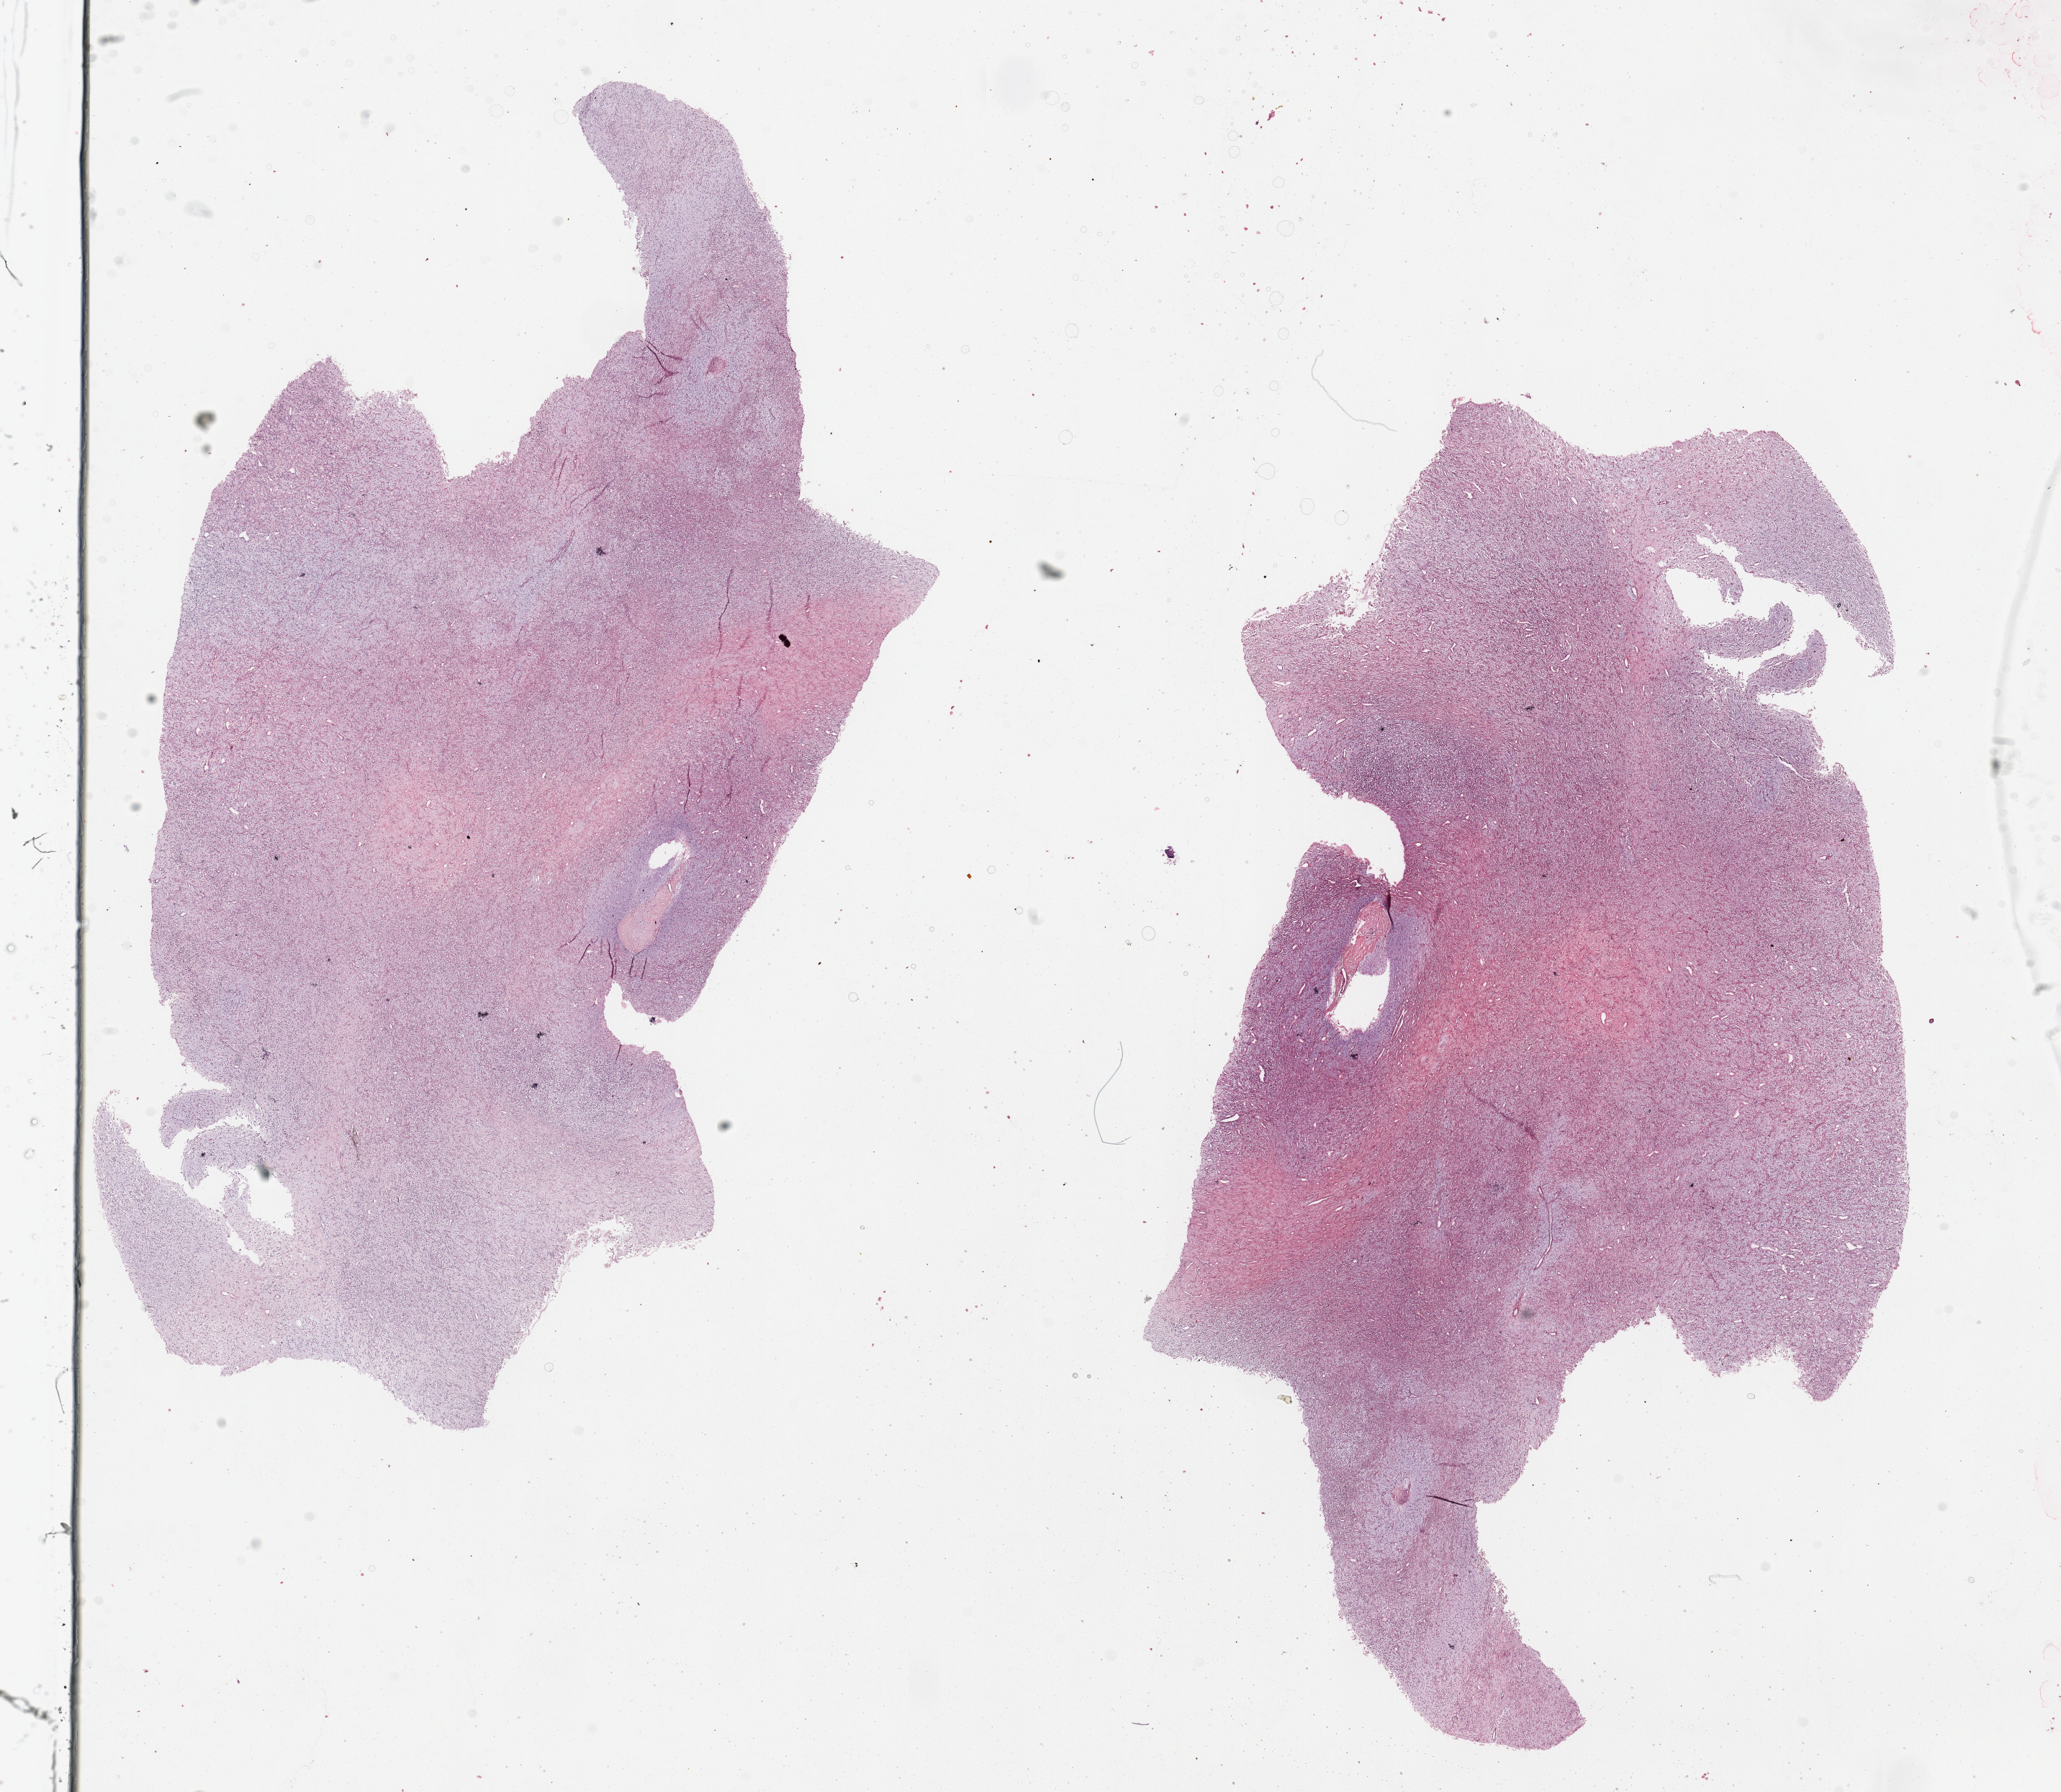
H&E-stained whole-slide image — shown as a low-resolution overview of the whole scanned area (about 22.6 x 19.7 mm), tumour tissue sample. 42-year-old male patient.
• patient diagnosis (cohort enrolment): sarcoma (site not recorded at cohort level)
• primary tumour site (as recorded): lower extremity